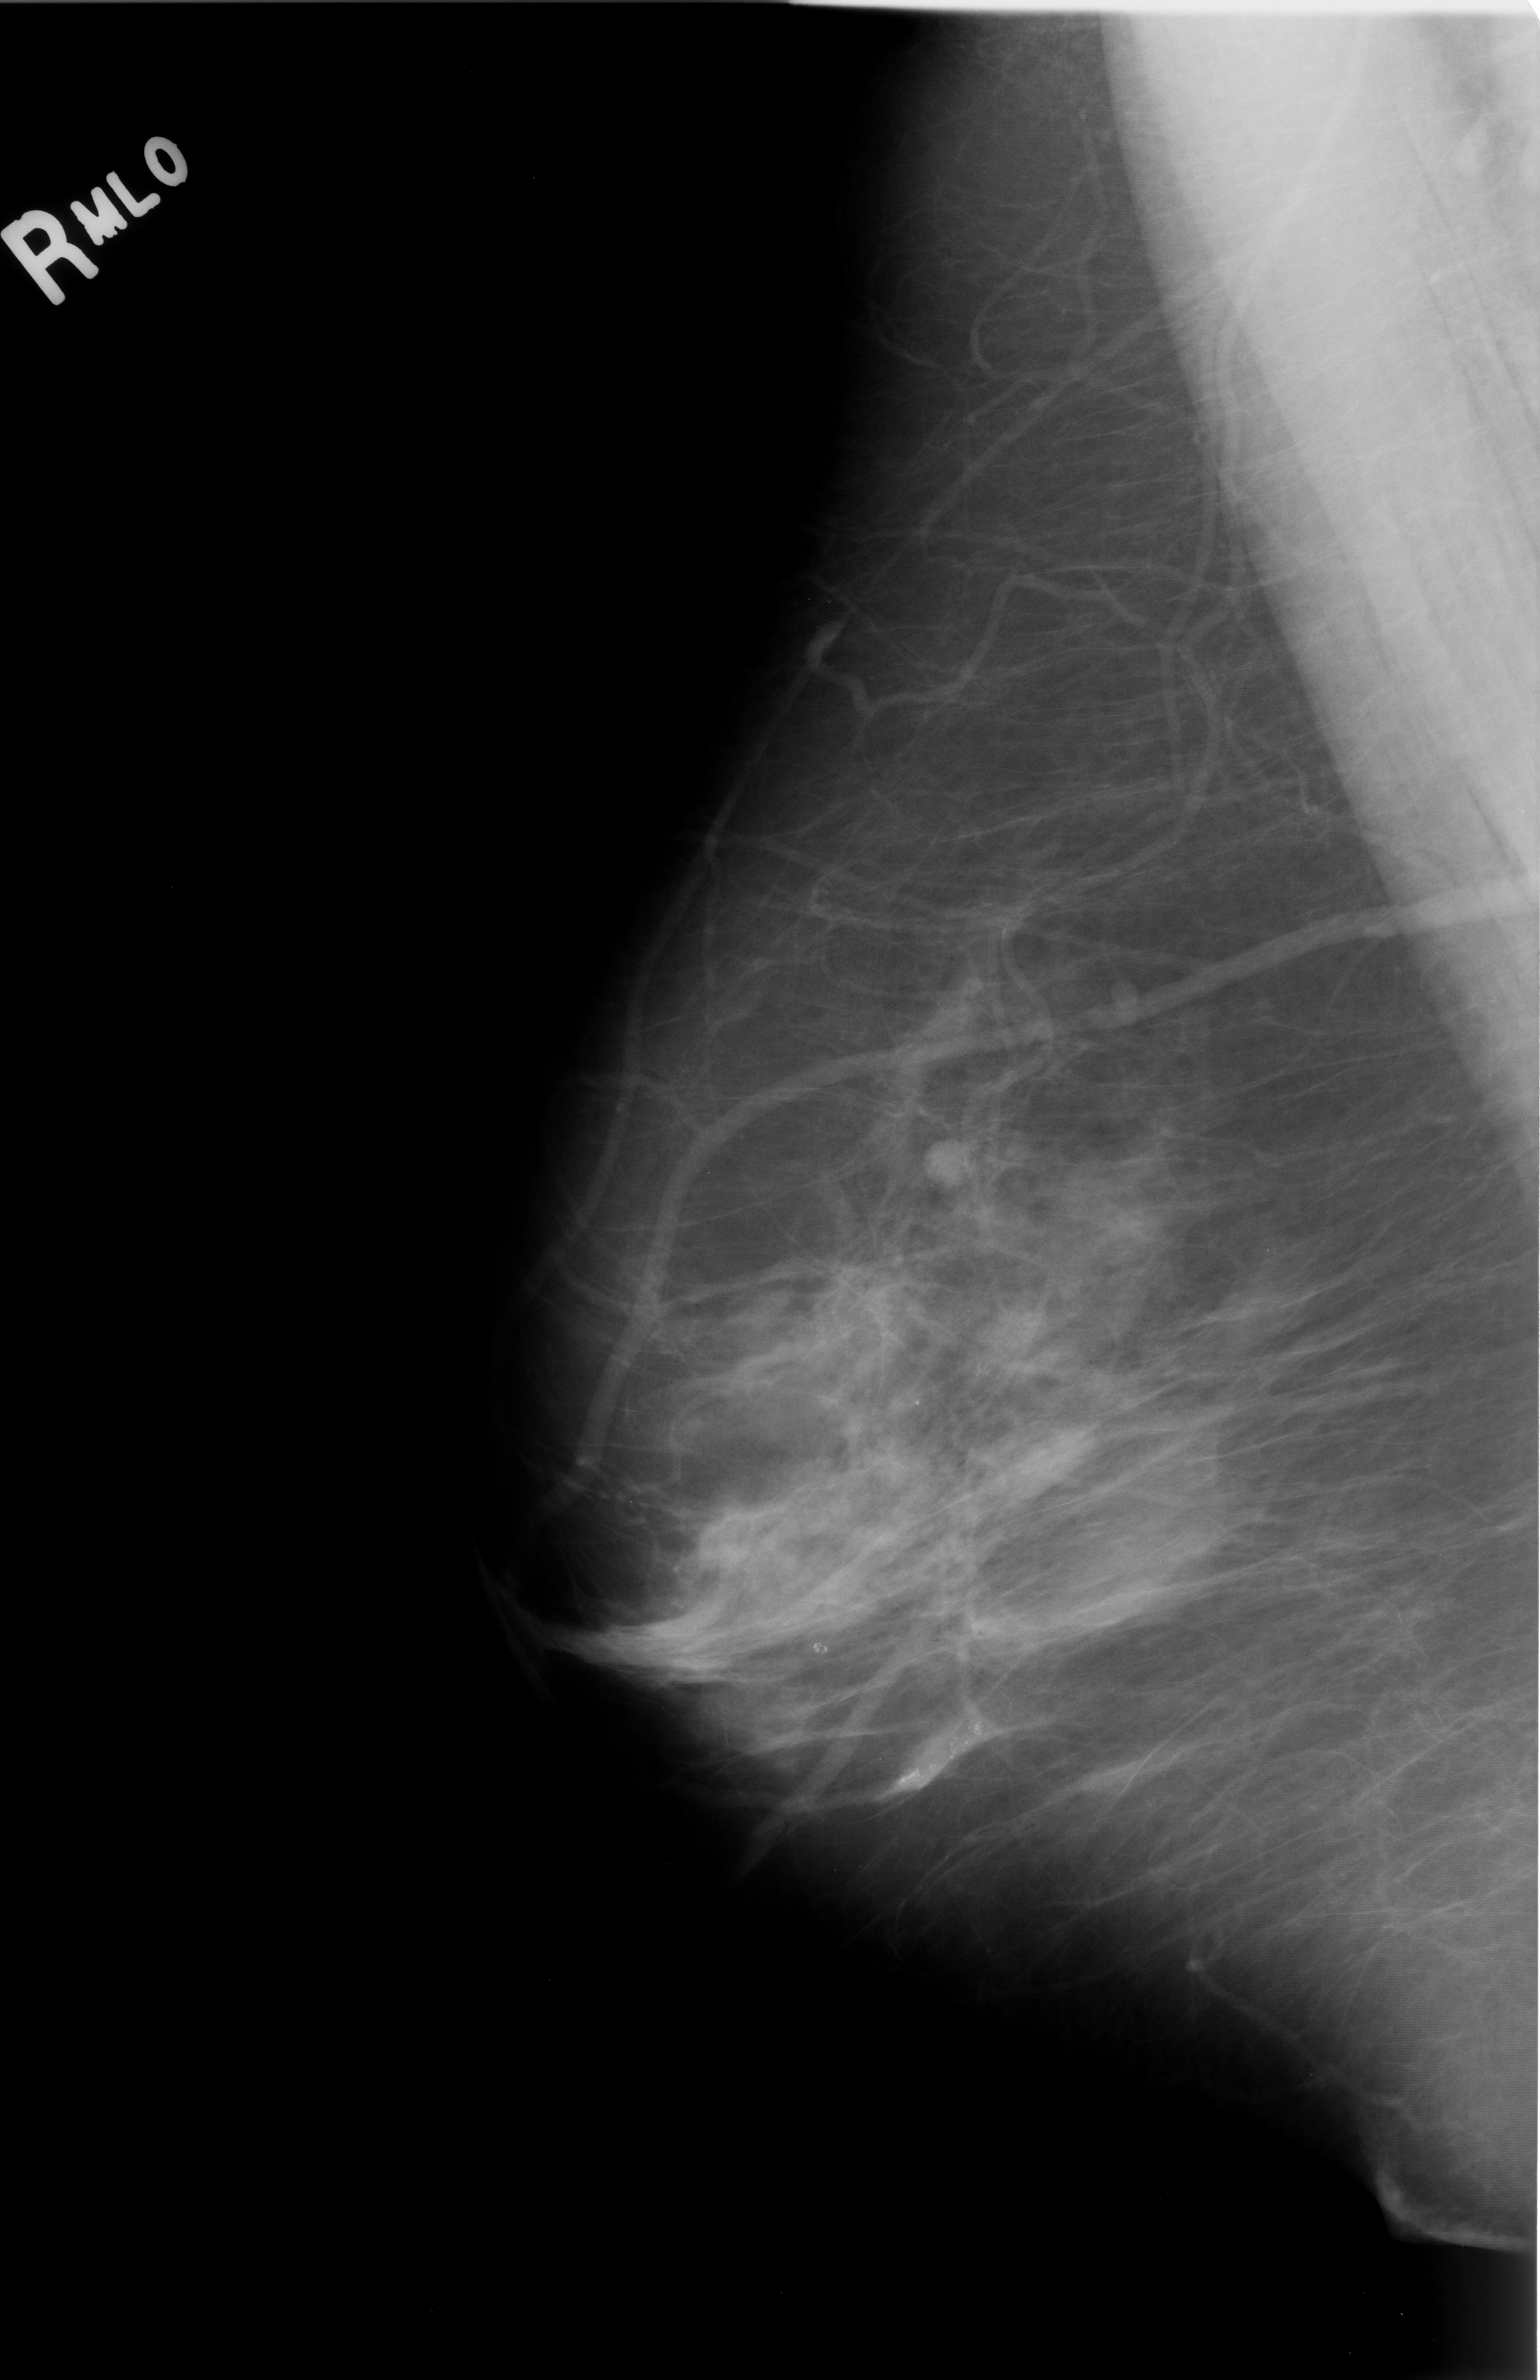
Digitized screen-film mammogram; right breast; mediolateral oblique (MLO) view; BI-RADS breast density category 2 (scale 1–4); 1540 × 2380 image matrix.
Marked abnormalities (boxes around the expert regions of interest):
- mass, shape round, margins circumscribed; BI-RADS assessment category 2; subtlety rating 5 on a 1 (subtle) to 5 (obvious) scale; outcome (as recorded, no biopsy): benign without callback (not worked up further): box from (x=912, y=1110) to (x=1014, y=1195) px